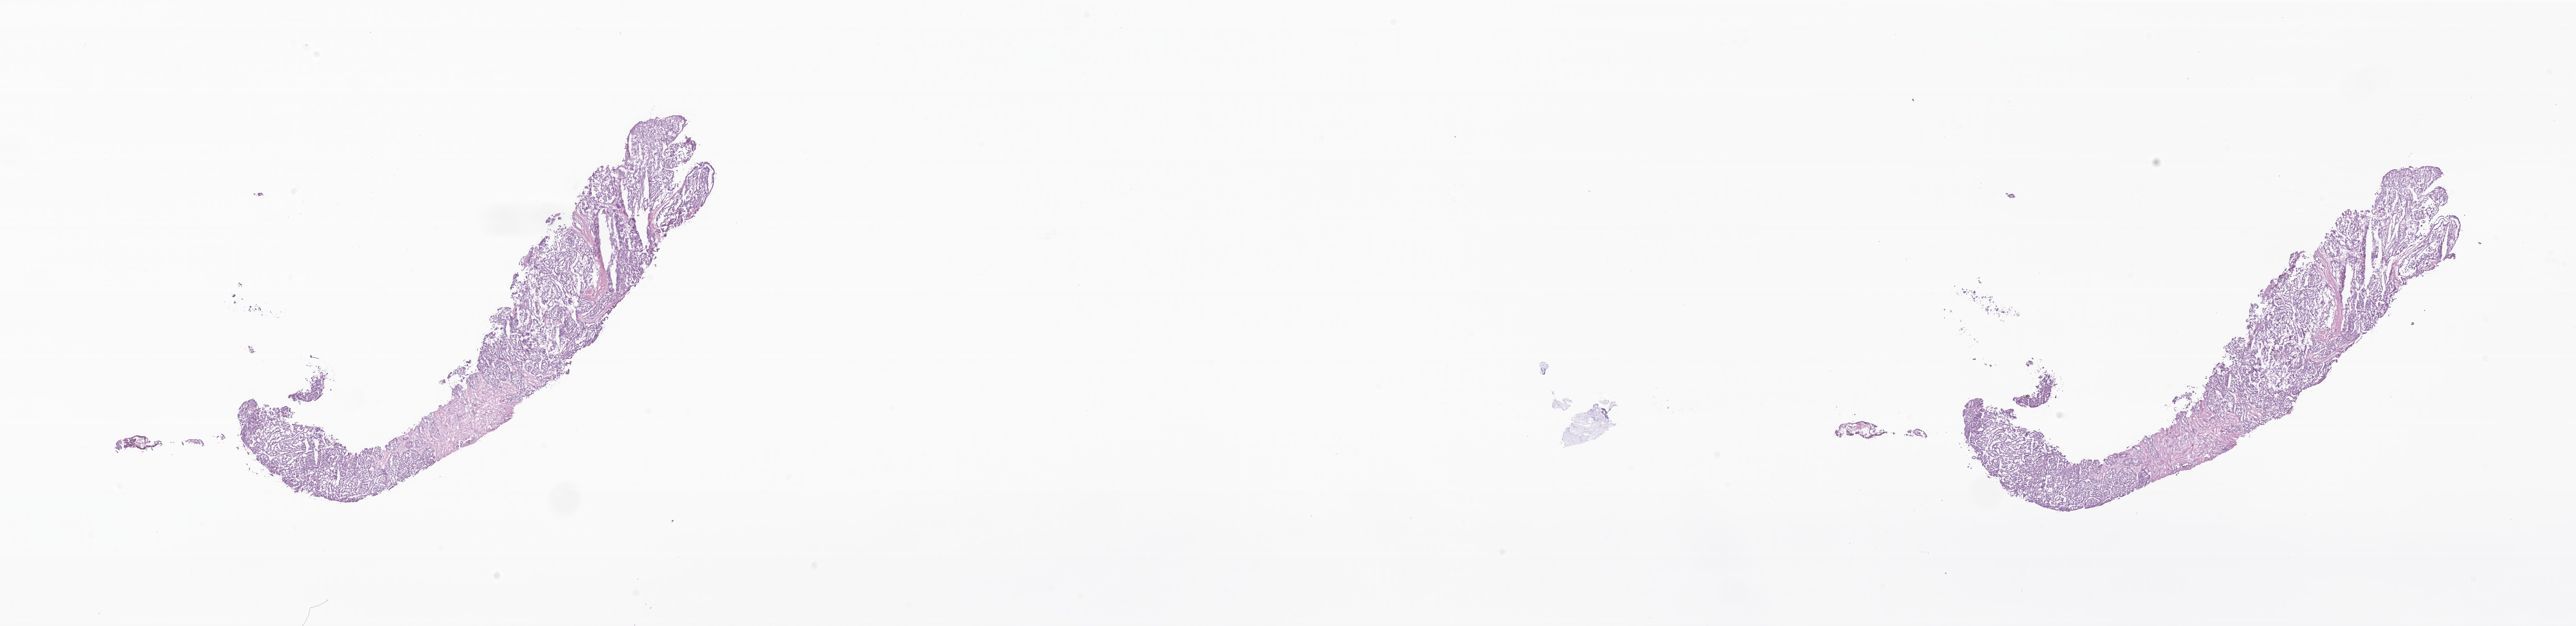
Hematoxylin and eosin (H&E) whole-slide image of tumor tissue from the thyroid, a low-resolution overview of the entire scanned area, about 41.5 x 10.1 mm; frozen section. Patient male; age 164 months (13 years 8 months).
* recorded diagnosis: Papillary carcinoma, NOS